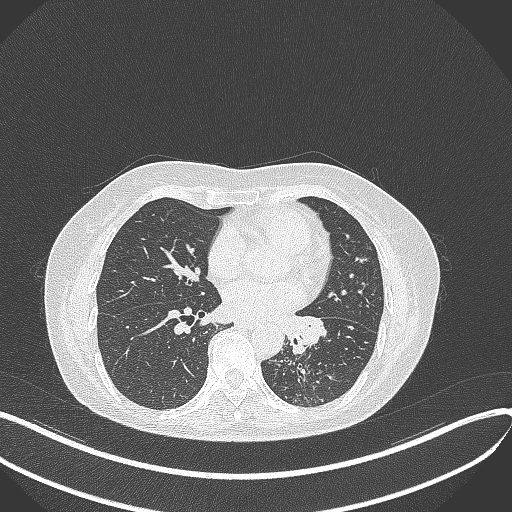
Chest CT, one axial slice; slice 187 of 429 in the series (ordered by position); lung window (W 1500 / L -600 HU); 1 mm slice thickness; 512 × 512 image matrix, field of view 400 × 400 mm. Patient: female, 63 years. Case-level facts recorded for this patient, not image findings: clinical TNM (as recorded): T1b N0 M0; histopathological grade: G2-3.
Annotated regions visible in this slice (rectangle marked by the reading radiologist):
- lung tumour (recorded histology: adenocarcinoma): bounding box [x1, y1, x2, y2] px = [284, 307, 328, 356]